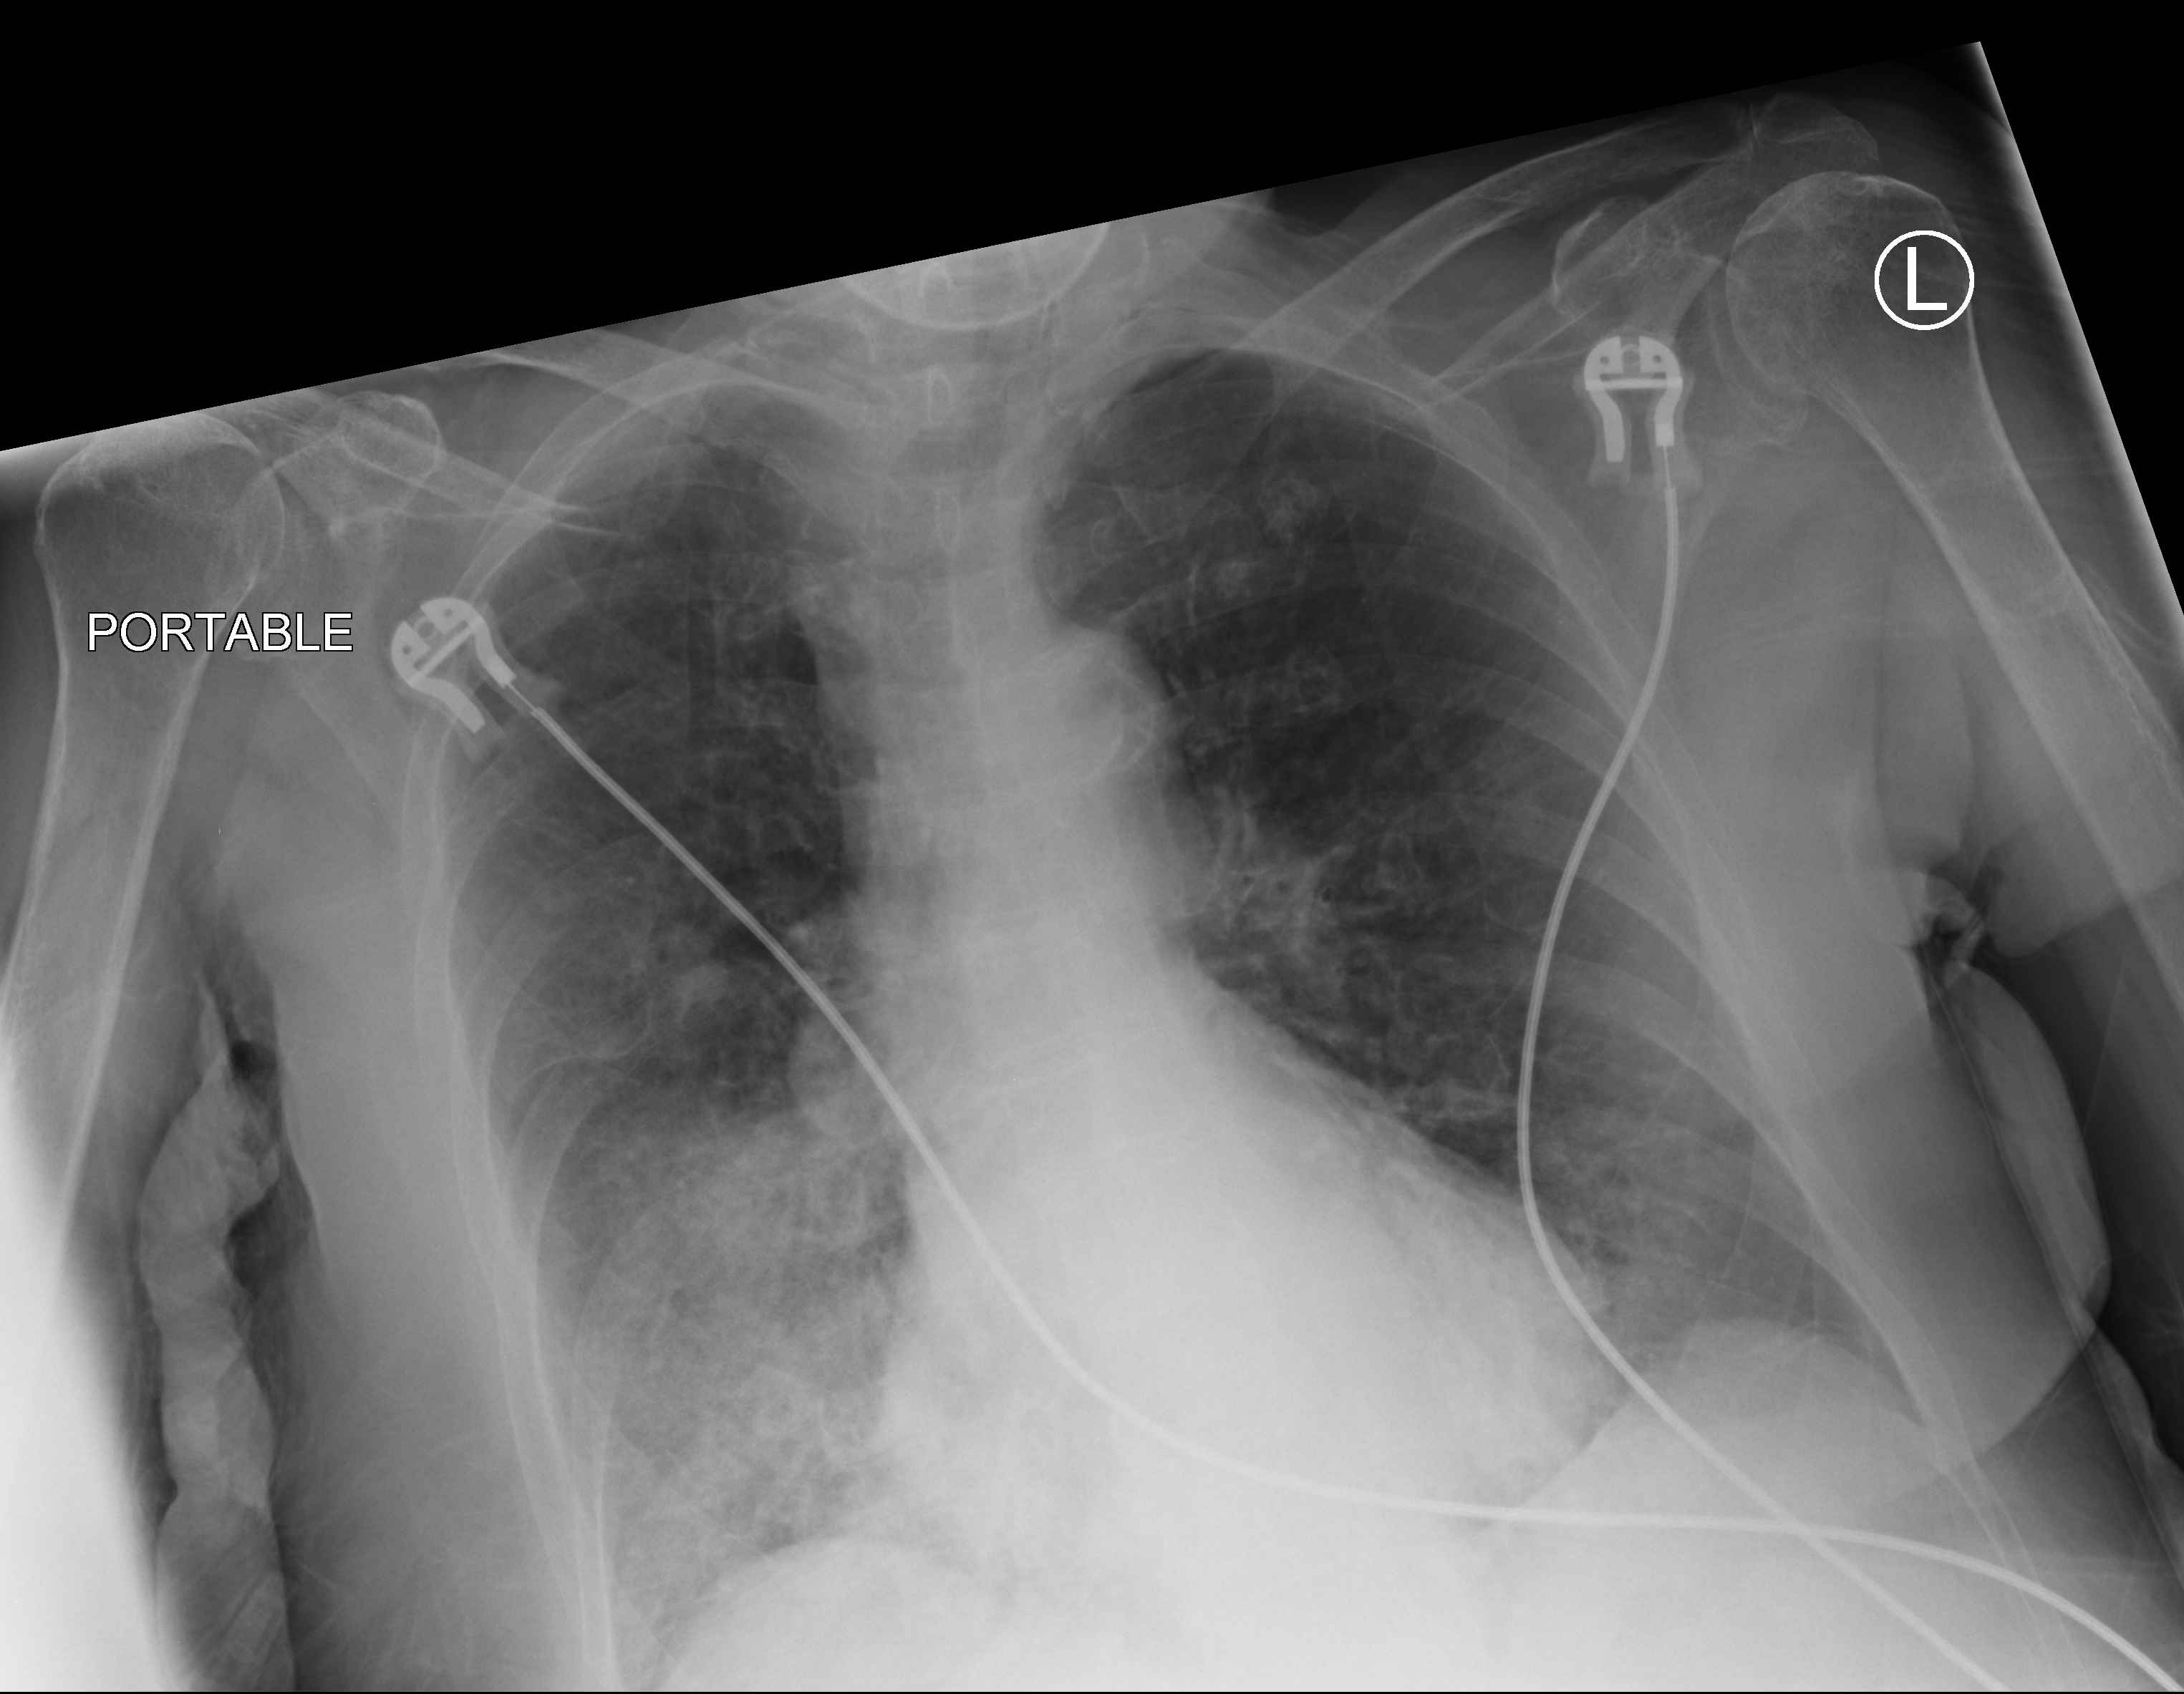
Portable chest radiograph, anteroposterior (AP) projection. Female patient hospitalised with COVID-19, age 75–90 years.
Hospital-stay facts (about this admission, not read from this image; timing relative to this image not recorded): admitted to intensive care during this hospital stay: no.